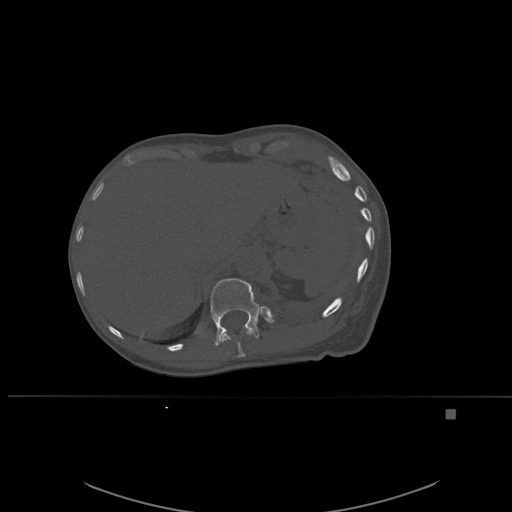
CT including the spine, one axial slice. Slice 287 of 537 in the series (ordered by position). Bone window (W 1800 / L 400 HU). 1.5 mm slice thickness. 512 × 512 image matrix, field of view 440 × 440 mm. Patient: female, 45 years. From the clinical record (not read from this slice): primary cancer: lung.
Outlined on this slice (semi-automatically segmented with operator editing):
- T11 vertebra: box from (x=221, y=328) to (x=254, y=357) px
- T12 vertebra: (x=210, y=278)–(x=261, y=346)